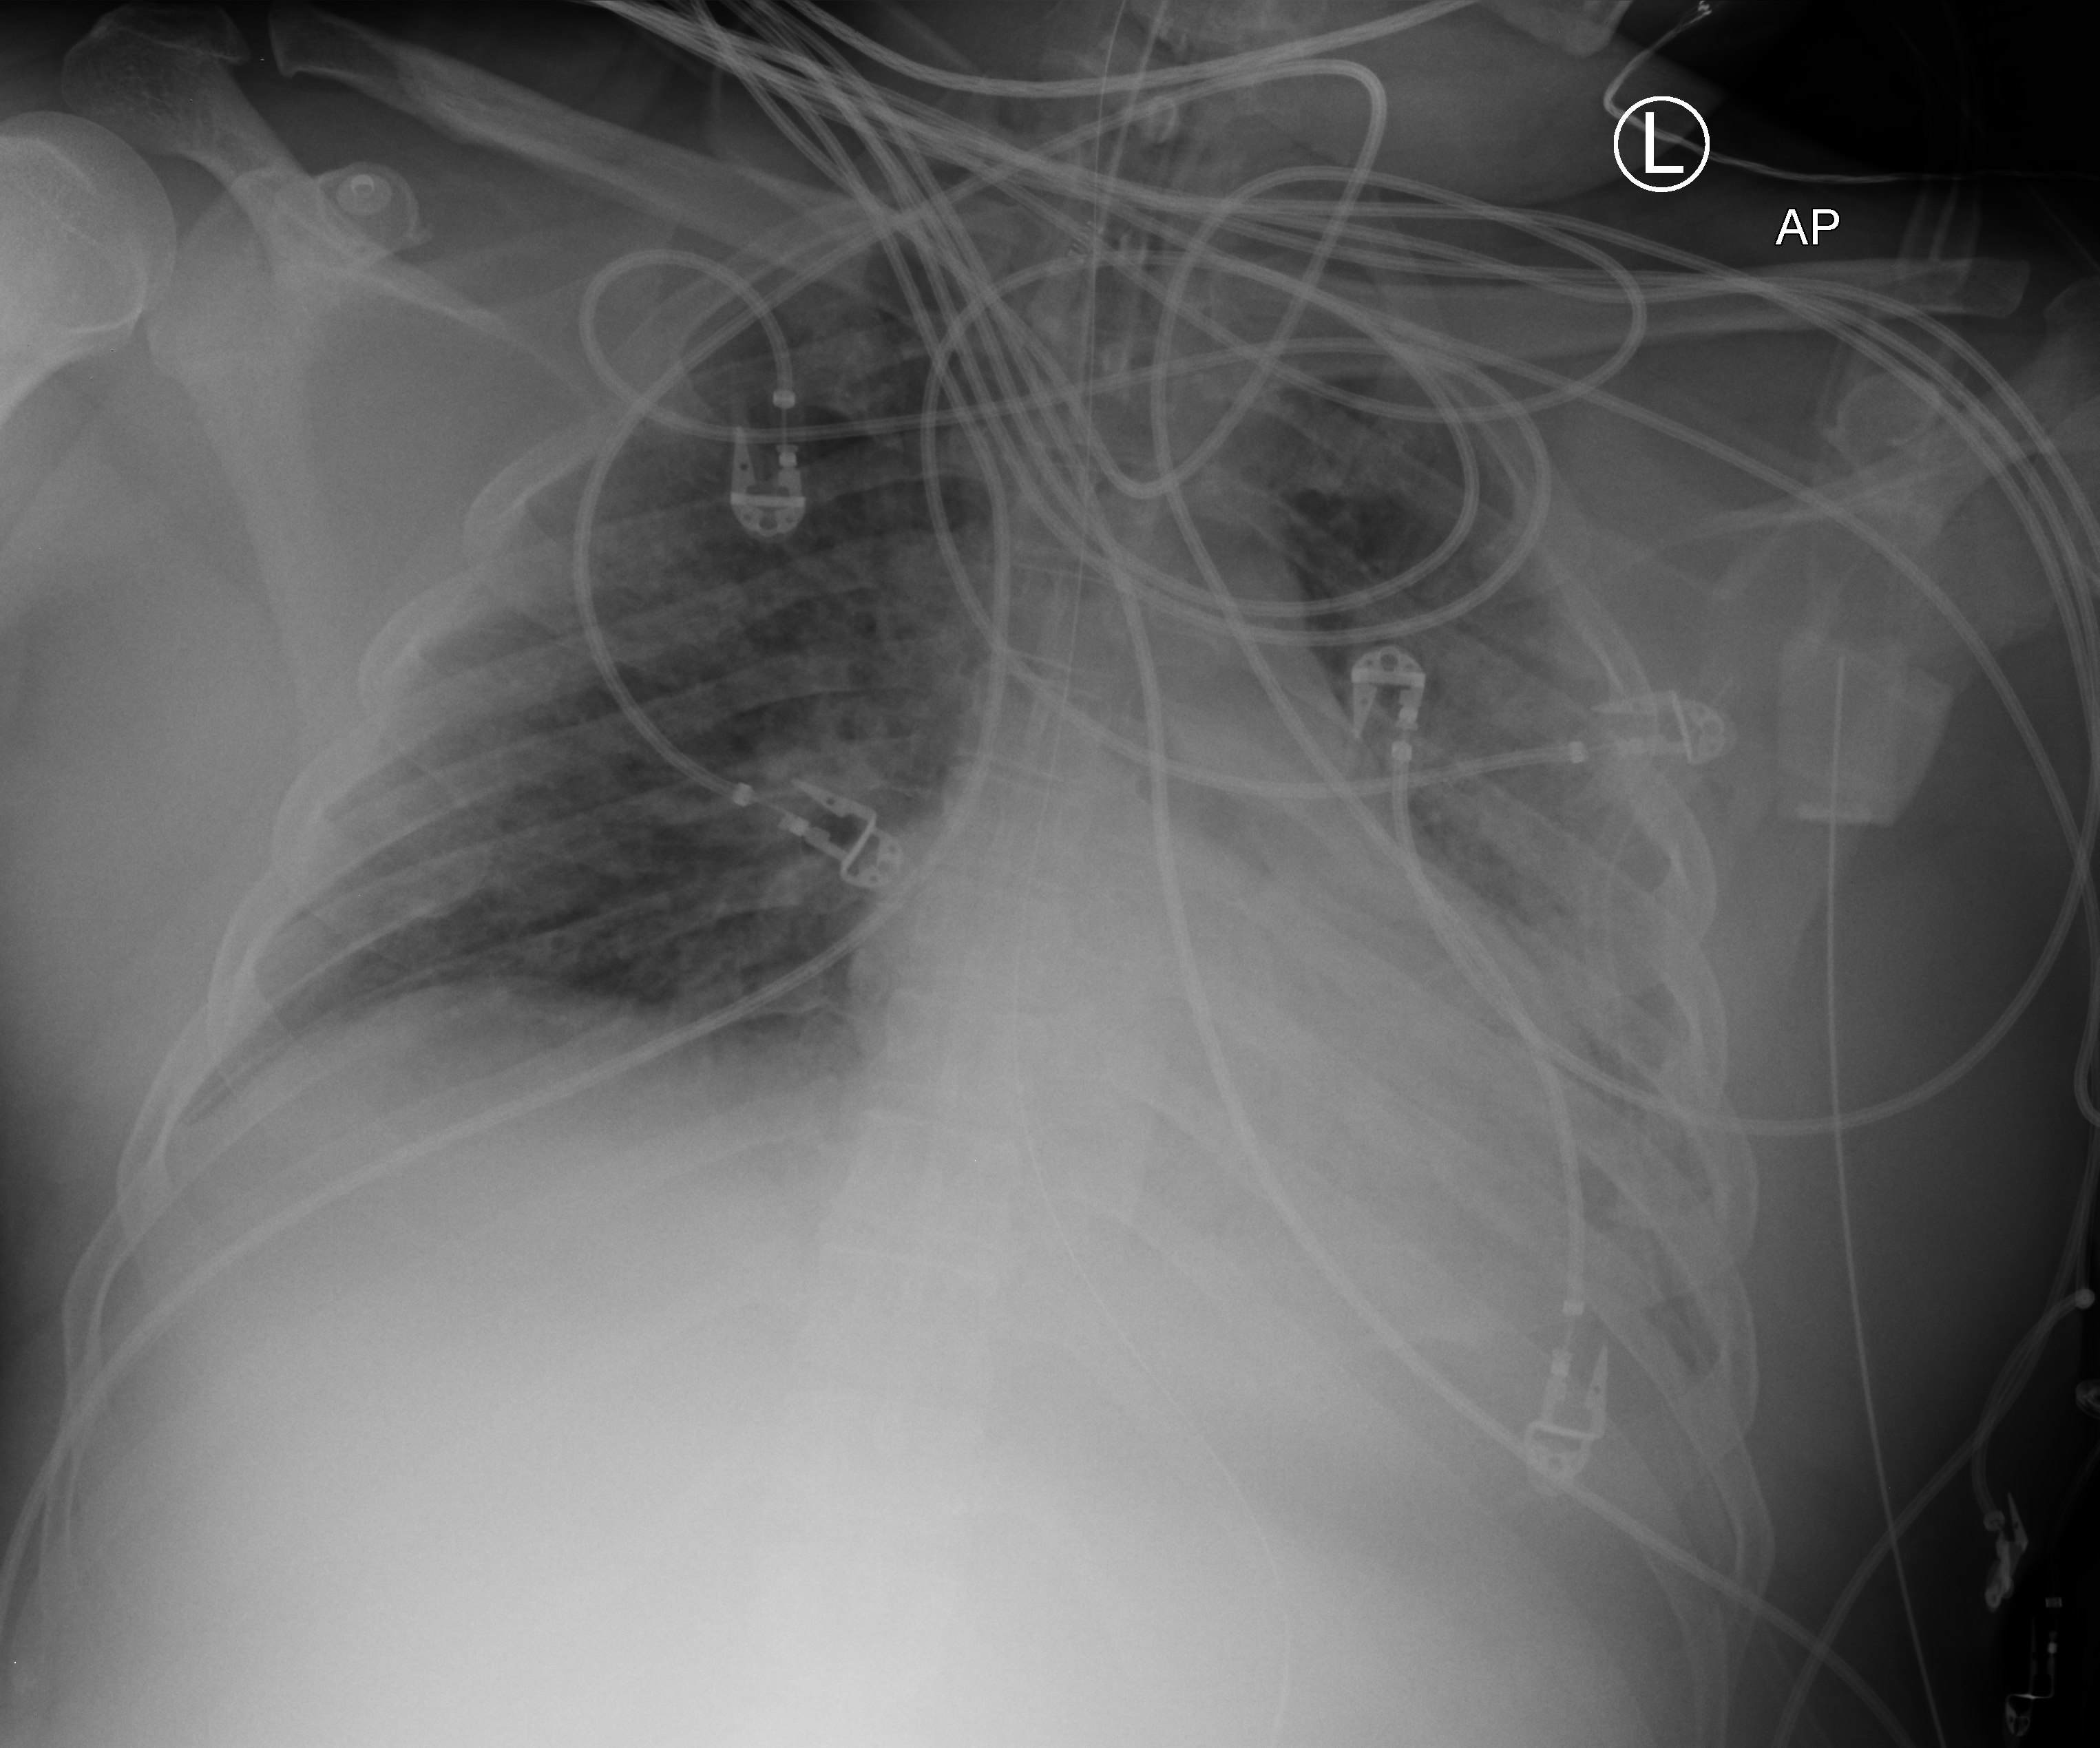
Chest X-ray (portable), anteroposterior (AP) projection. Patient hospitalised with COVID-19, aged 18–59 years.
Hospital-stay facts (about this admission, not read from this image; timing relative to this image not recorded): admitted to intensive care during this hospital stay: yes.